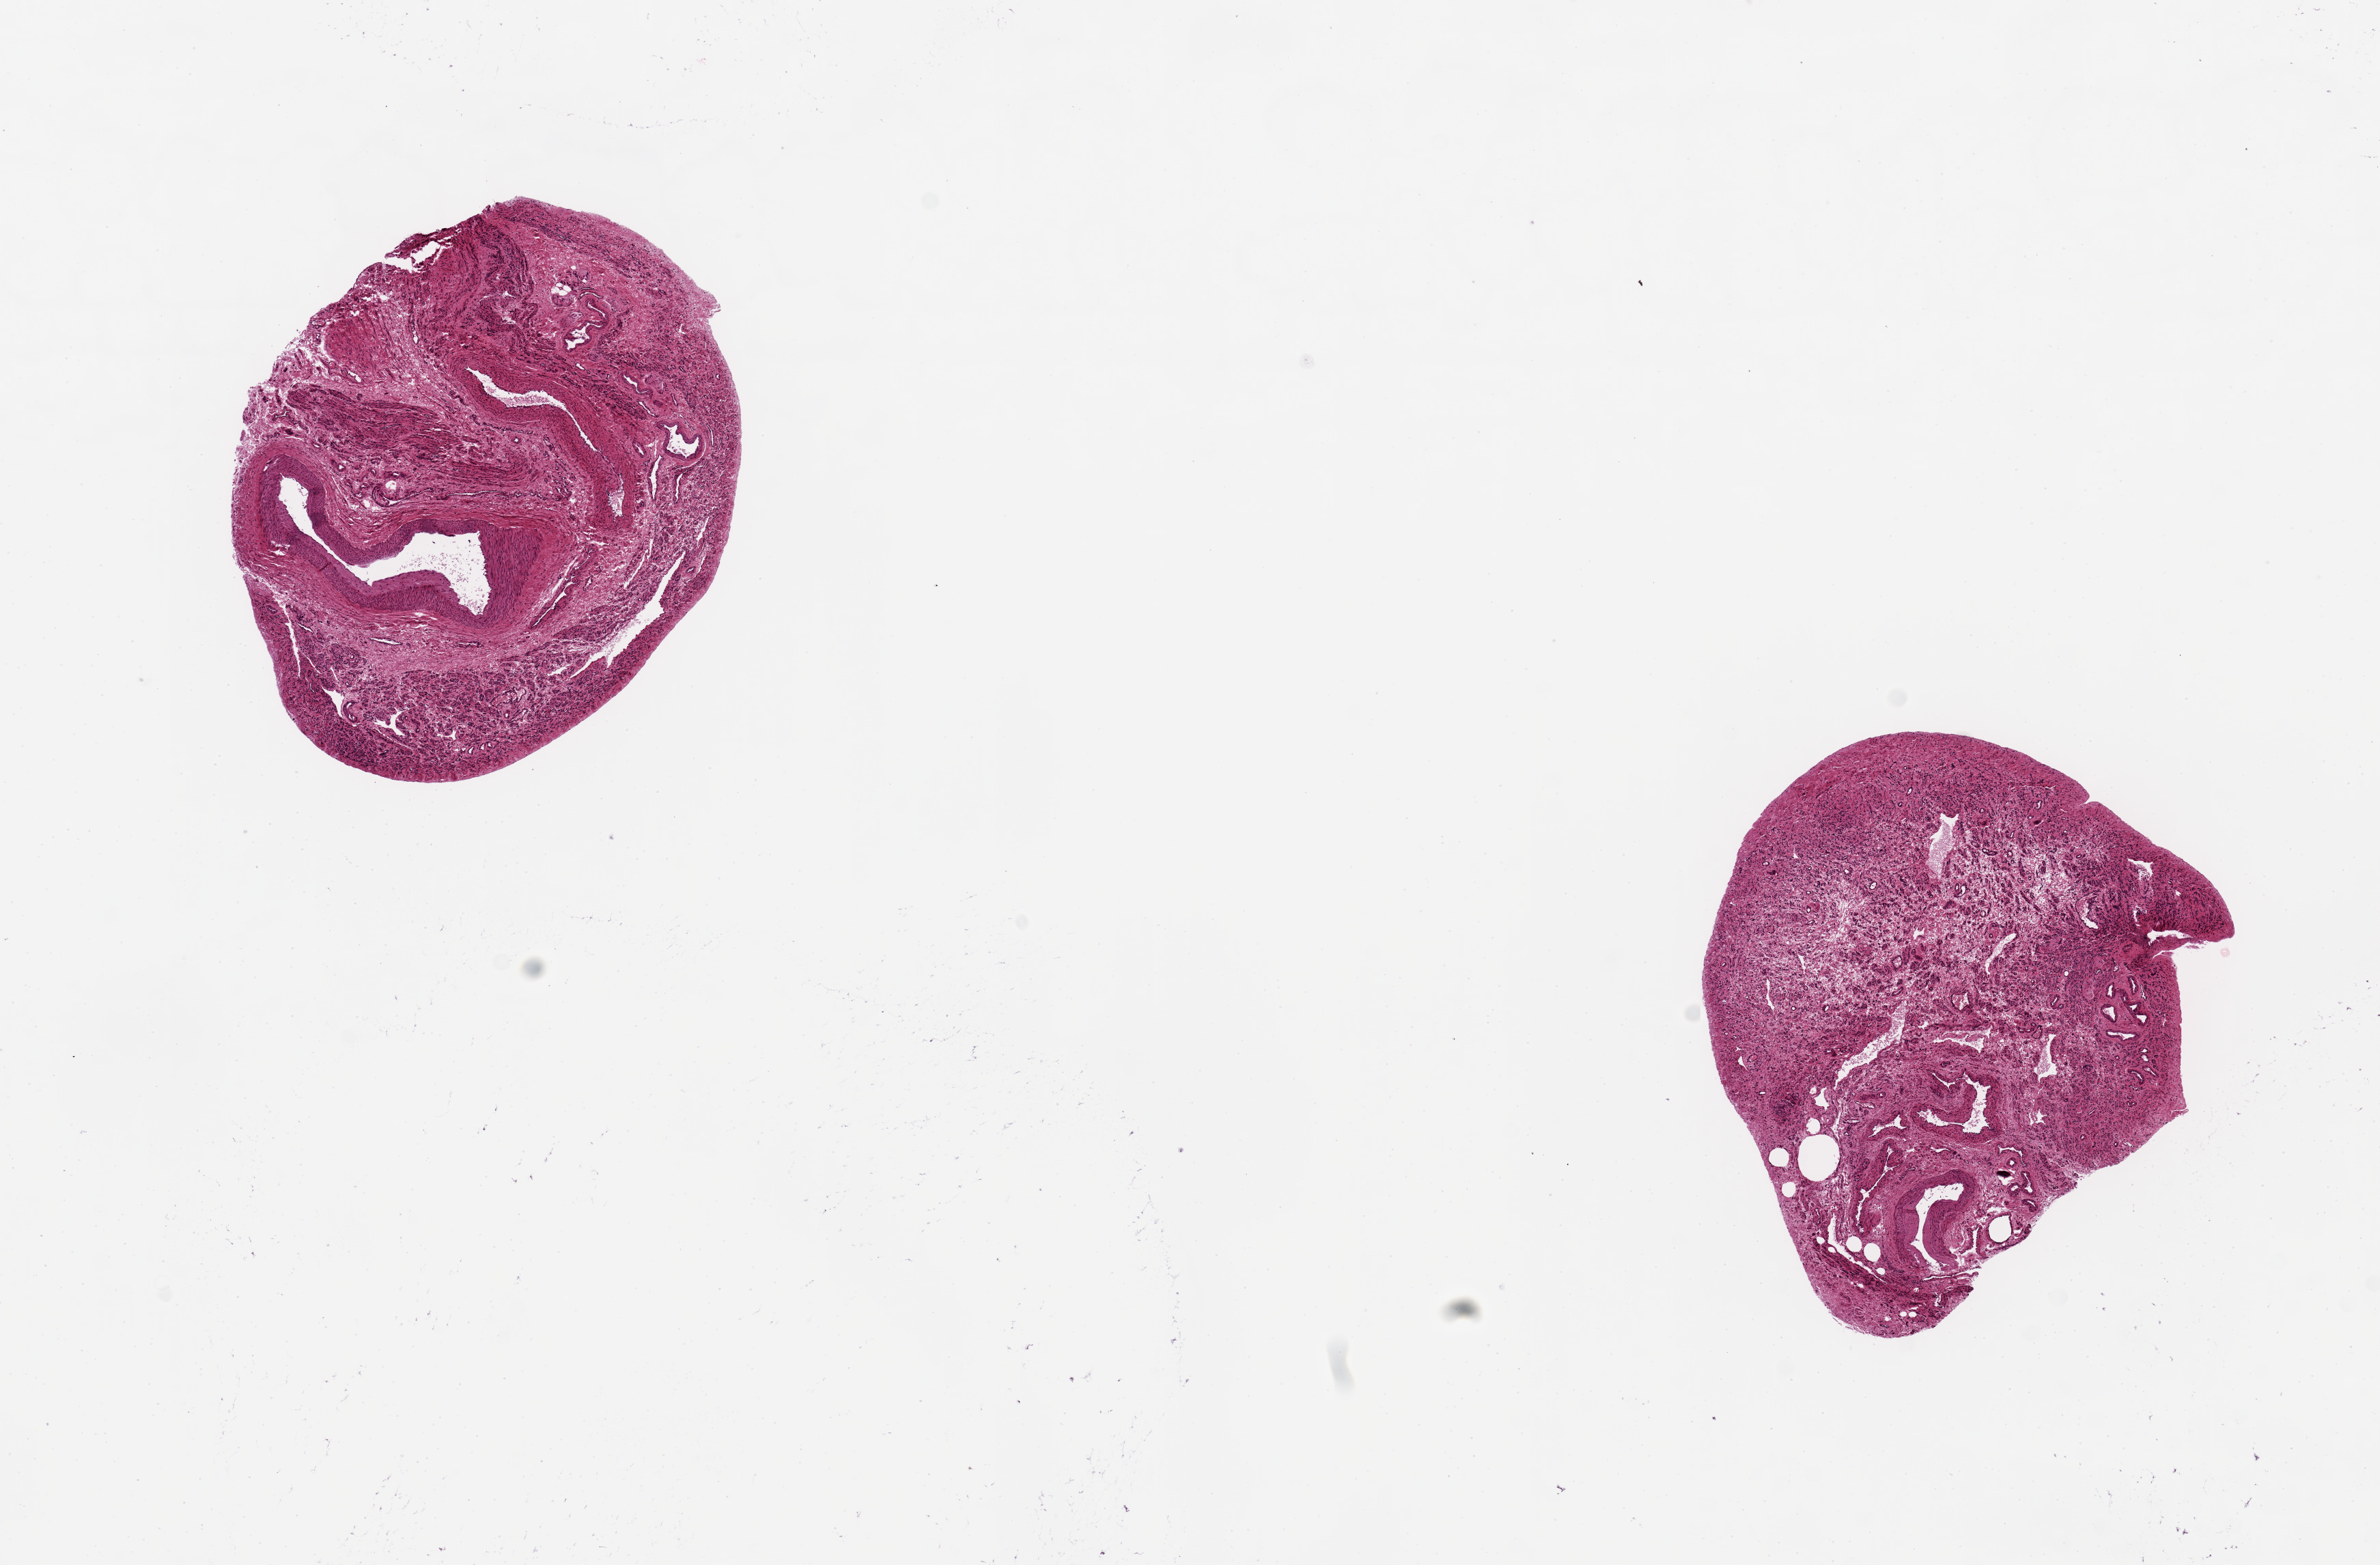
Whole-slide image, haematoxylin and eosin stain, whole scanned area (about 13.8 x 9.1 mm, from a 20x scan) shown as a low-resolution overview; PAXgene-fixed paraffin-embedded (PFPE) section; section of fallopian tube (target tissue); tissue donor sample. Female donor.
Pathologist's review note for this sample: Not tube, fibrovascular tissue.